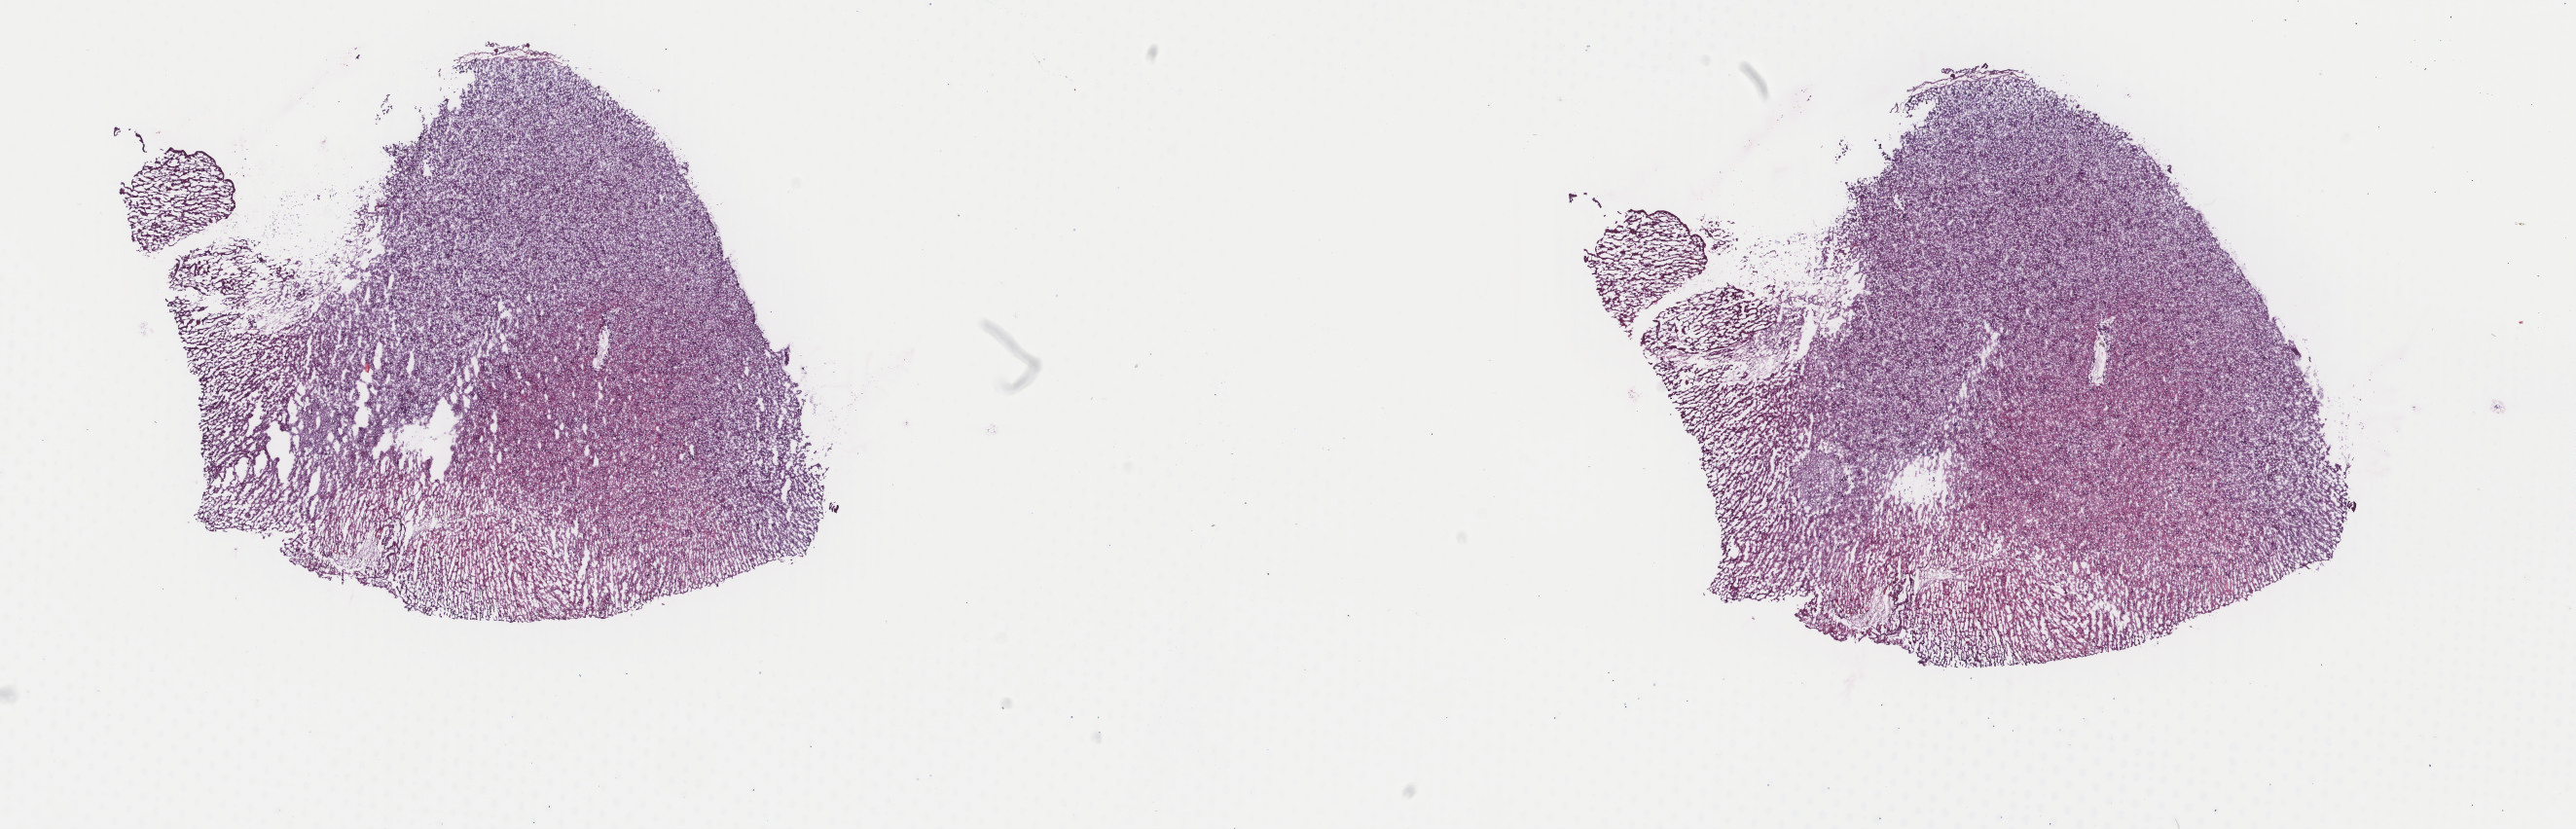
Whole-slide histology image, Hematoxylin and eosin (H&E) stained — low-resolution overview of the scanned area, about 21.0 x 6.8 mm, frozen section from the top of the tissue portion, recurrent tumour sample from the brain. Female patient; age at initial diagnosis 39 years. Composition of this section per pathologist review: tumour cells 60%, tumour nuclei 70%, normal cells 20%, stromal cells 0%, necrosis 20%. Inflammatory infiltration, as recorded: lymphocyte infiltration 0%, monocyte infiltration 0%, neutrophil infiltration 0%.
This section: recurrent tumour. Patient diagnosis: Mixed glioma.